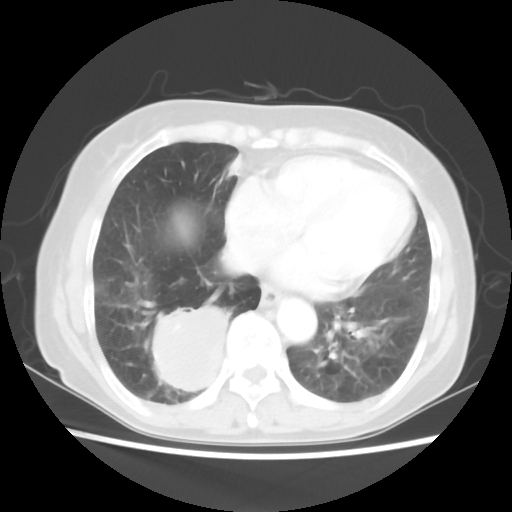
Chest CT, one axial slice; position 22 of 56 along the scan axis; lung window (W 1500 / L -600 HU); 512 × 512 image matrix. Patient: female, 66 years. Case-level facts recorded for this patient, not image findings: clinical TNM (as recorded): T2 N3 M0; histopathological grade: G3.
Outlined on this slice (bounding box drawn by a radiologist):
- lung tumour (recorded histology: small cell carcinoma): bounding box [x1, y1, x2, y2] px = [148, 300, 239, 400]